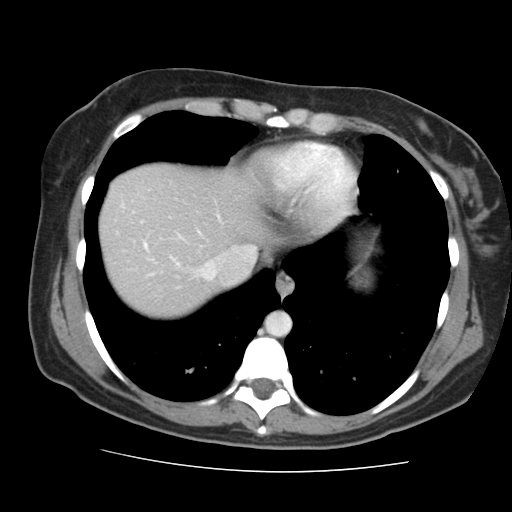
Contrast-enhanced abdominal CT, one axial slice. Position 132 of 144 along the scan axis. 120 kVp. Intravenous contrast given. Soft-tissue window (W 400 / L 40 HU). 2.5 mm slice thickness. 512 × 512 image matrix, field of view 333 × 333 mm. Female patient, age 46 years. From the clinical record (not read from this slice): diagnosis: colorectal cancer liver metastases, imaged before liver resection; multiple liver metastases: no; largest metastasis: 2.8 cm.
Outlined on this slice (outlined manually by an expert reader):
- hepatic veins: box from (x=197, y=246) to (x=255, y=280) px
- liver: (x=100, y=165)–(x=267, y=316)
- planned liver remnant (the part of the liver to remain after resection): (x=100, y=165)–(x=267, y=316)